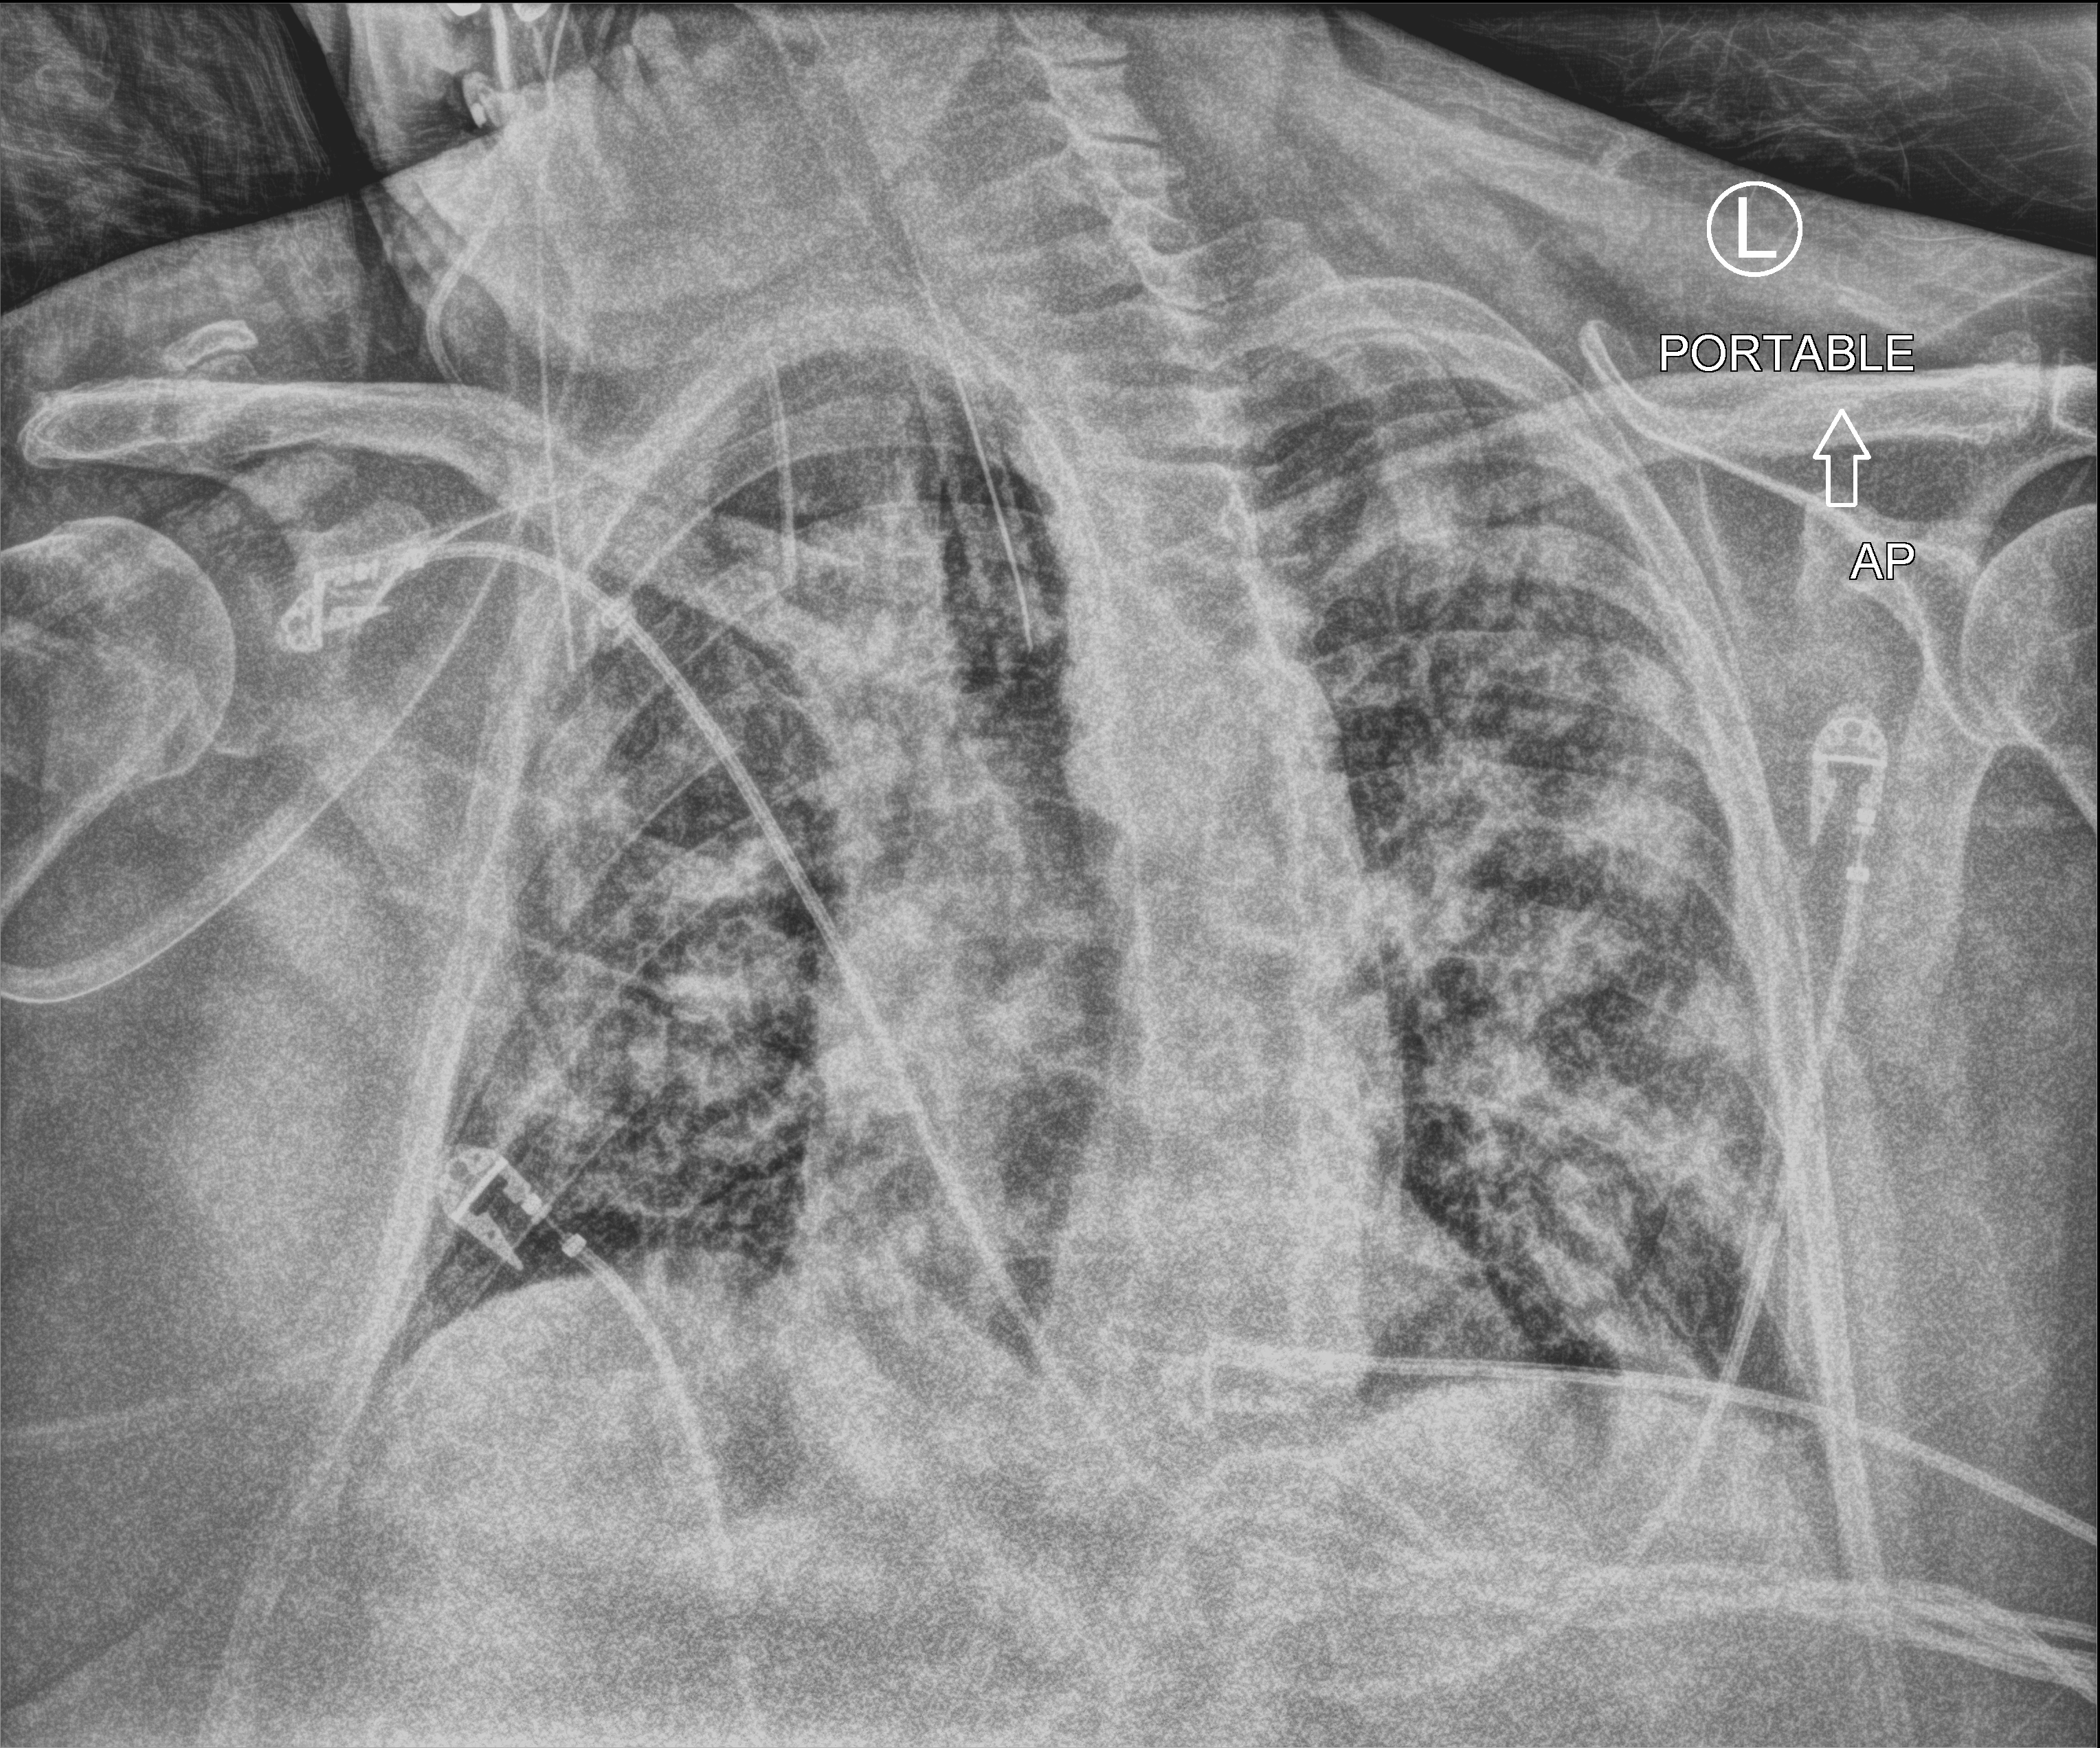
Bedside chest radiograph (computed radiography), anteroposterior (AP) projection. Male patient hospitalised with COVID-19, age 60–74 years.
From the hospital-stay record, not from the radiograph (when in the stay this image was taken is not recorded):
- mechanically ventilated during this hospital stay: yes